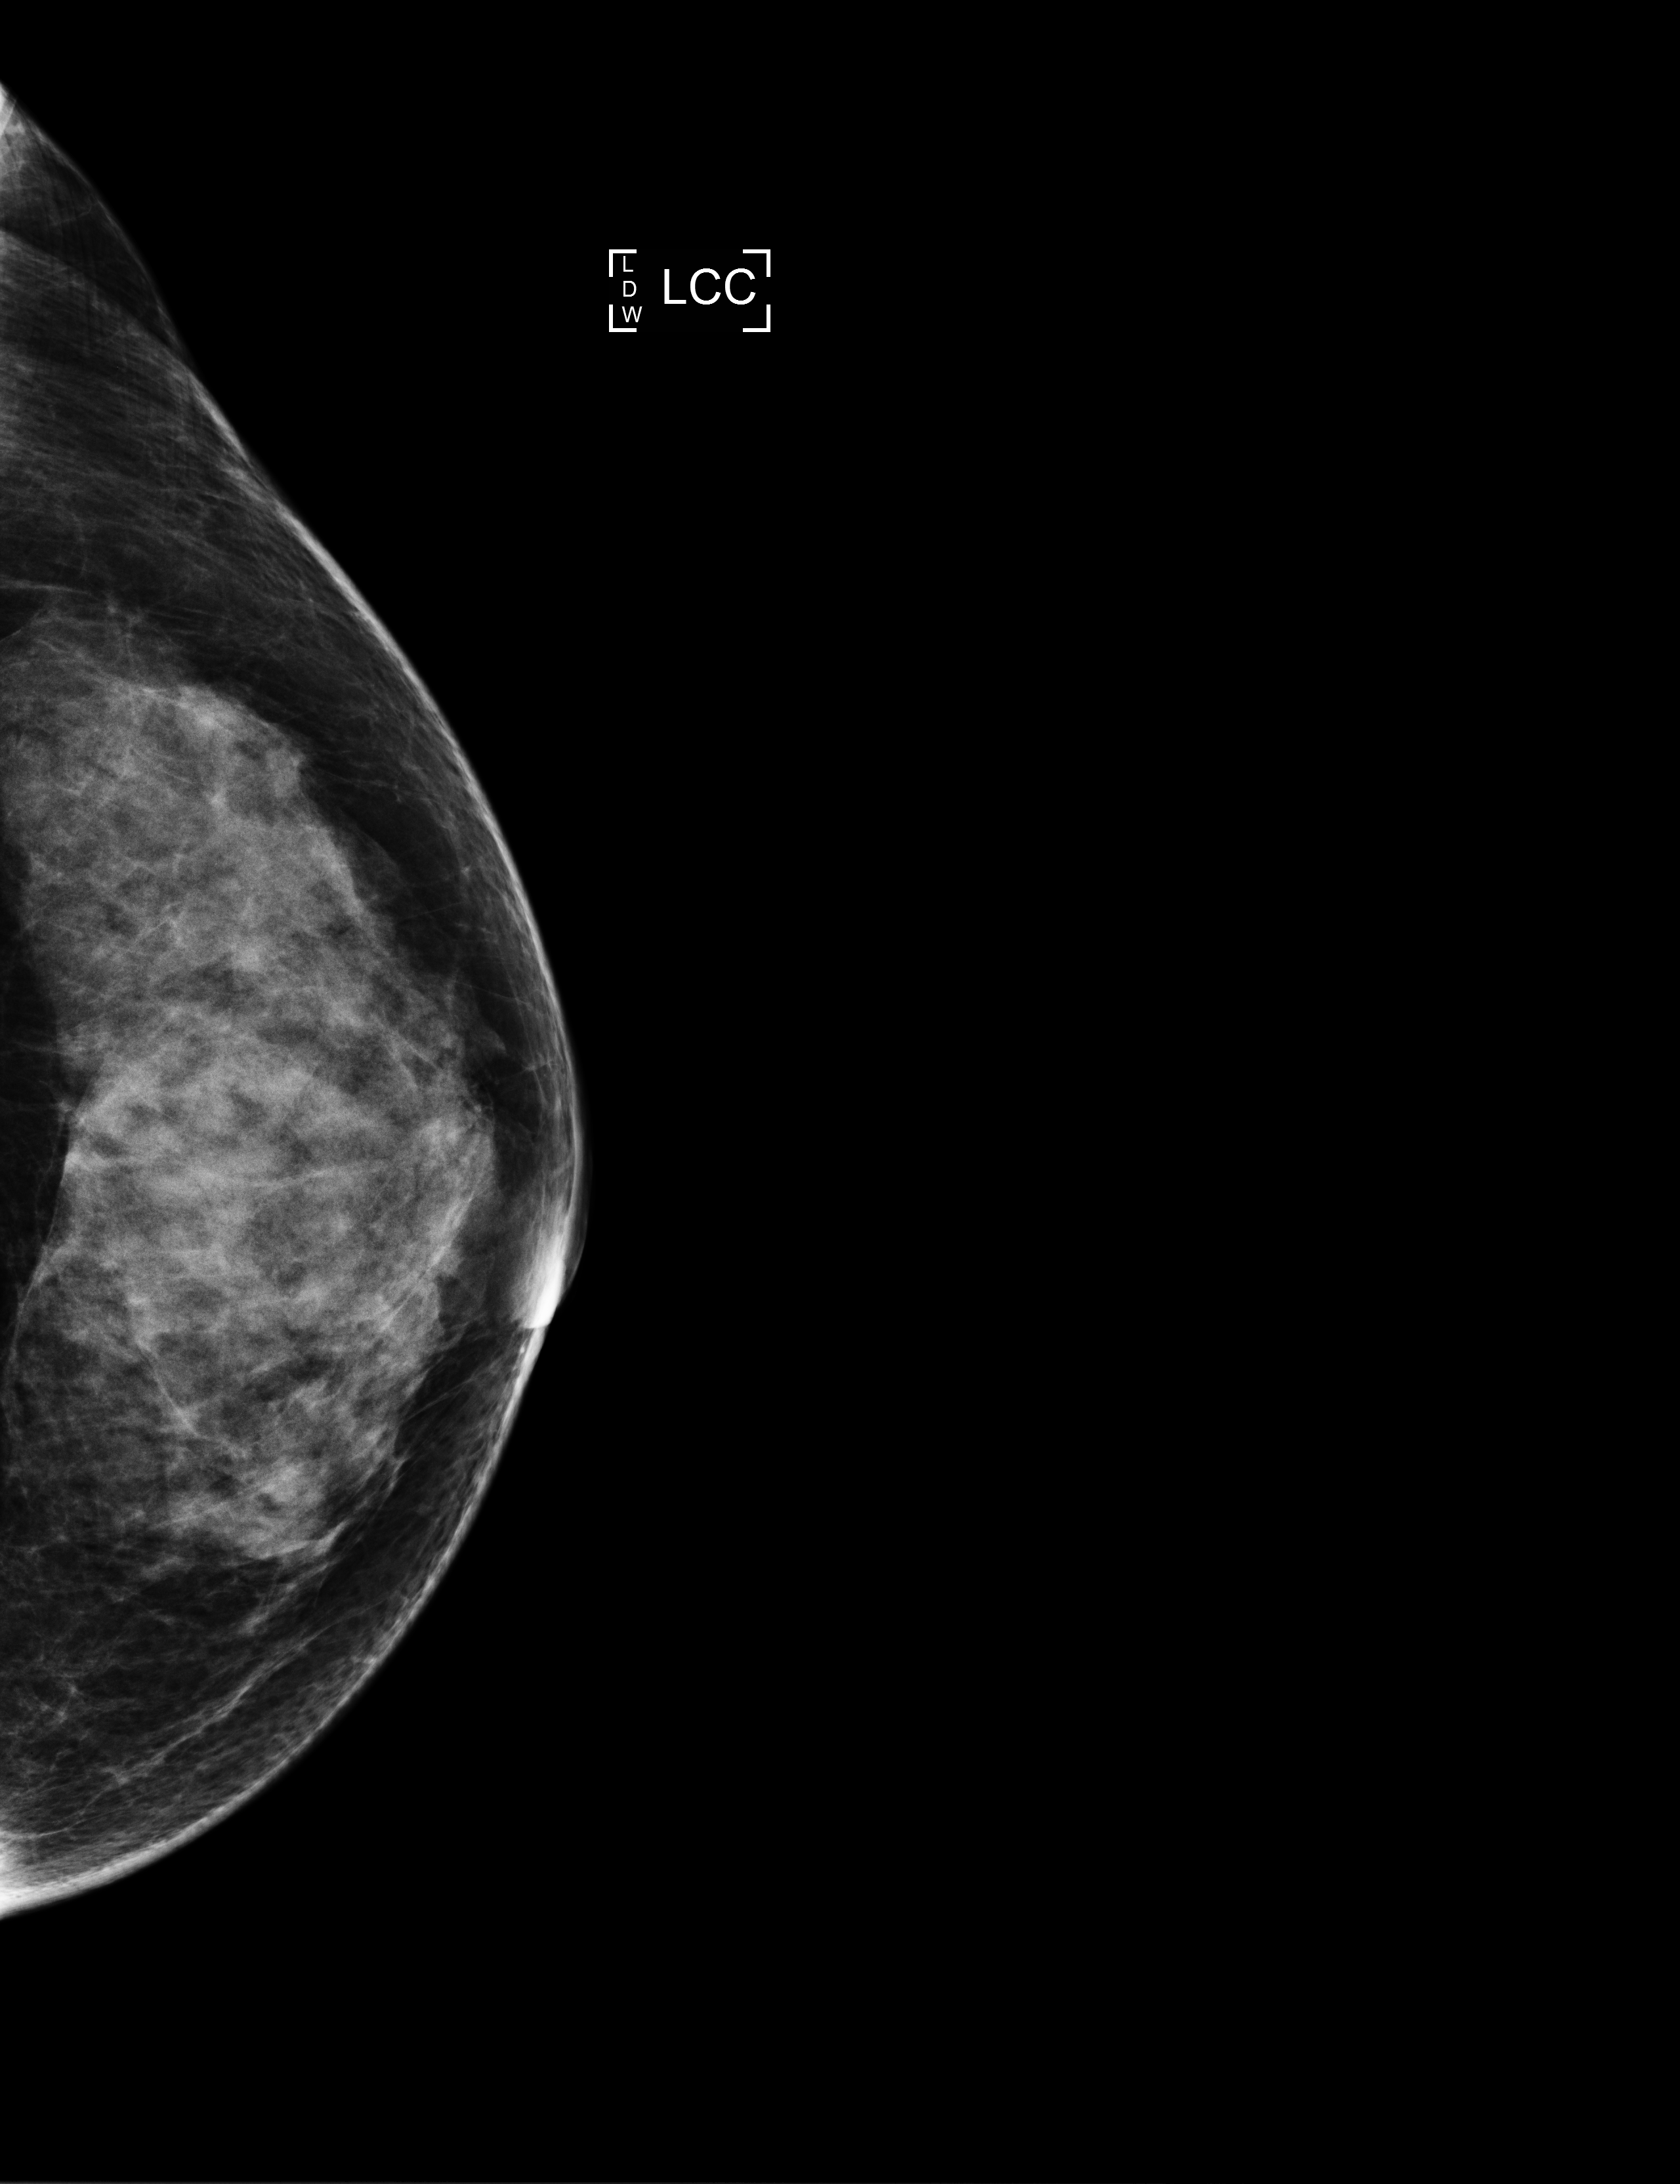
Digital mammogram (FFDM); left breast; cranio-caudal projection; annual screening mammography examination; system: Selenia Dimensions. Patient: female, 50 years.
BI-RADS breast density category at the screening exam (both breasts, scale 1–4): 4. Final BI-RADS assessment for this screening round (tomosynthesis exam, both breasts): category 1. Recall: no recall after this screen.